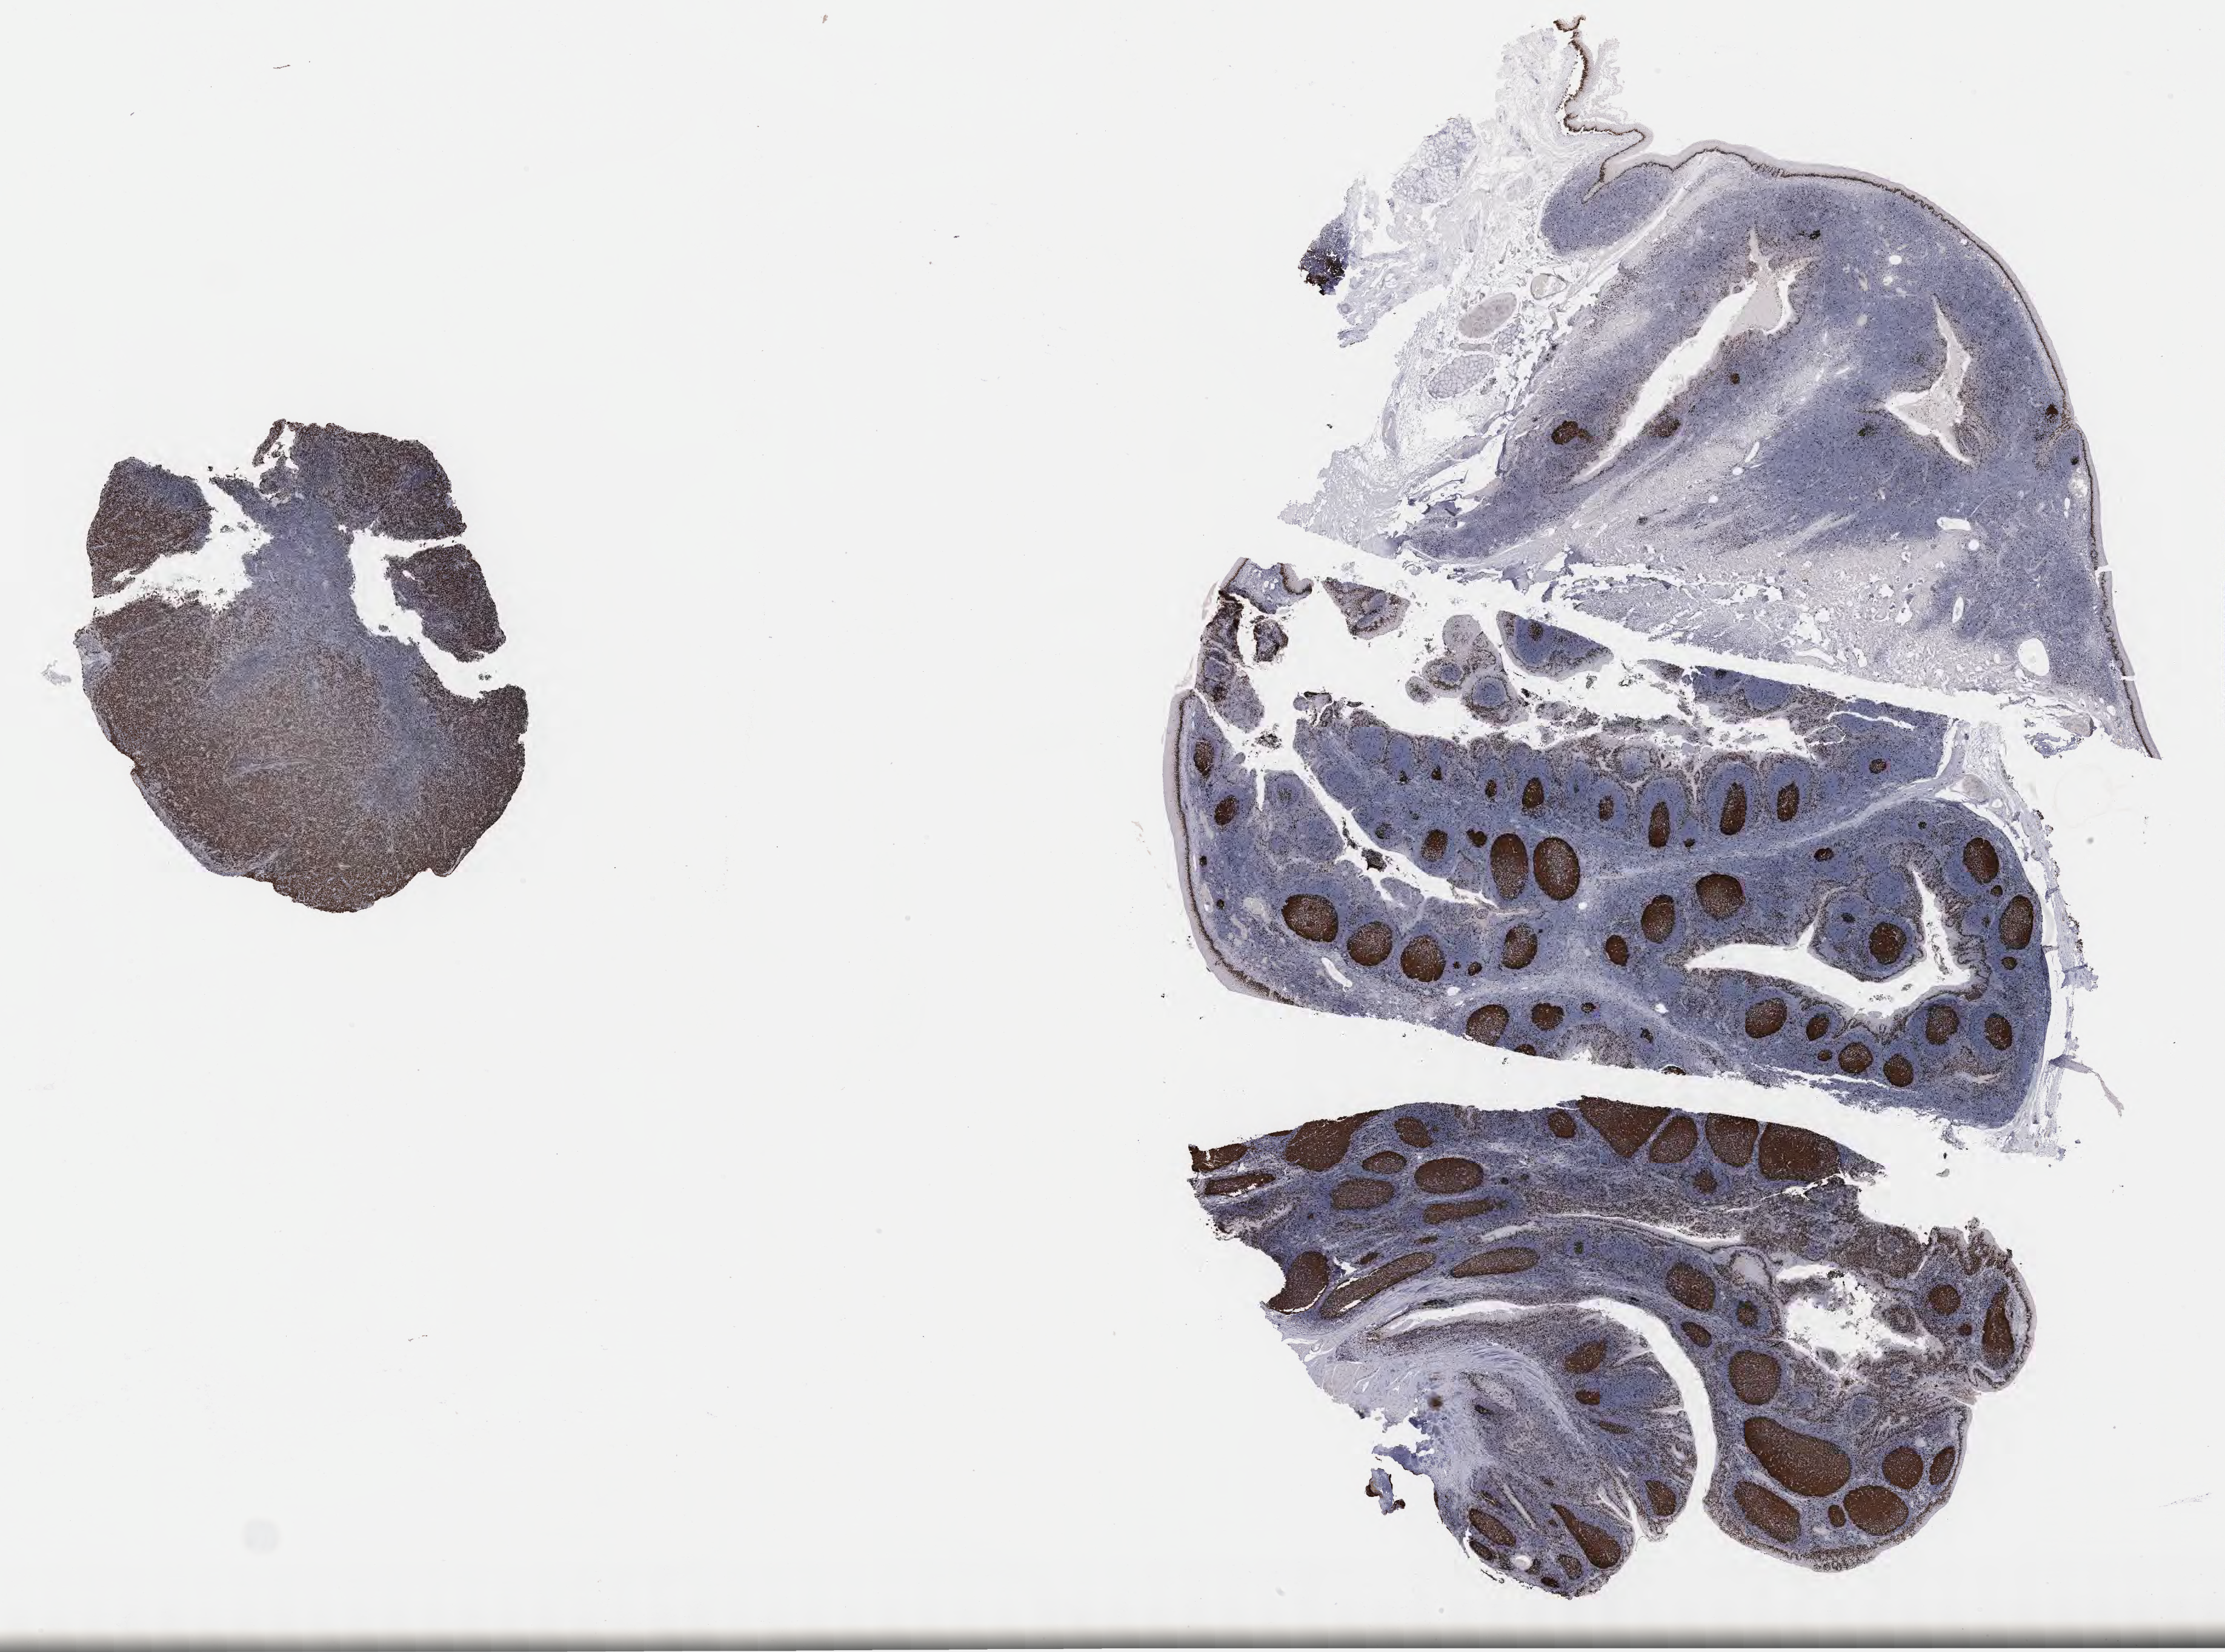
IHC for Ki-67, whole-slide image — shown as a low-resolution overview of the whole scanned area (about 29.7 x 22.1 mm). Tumor tissue. Anatomic site: liver. Patient male; 46 years old.
Histologic diagnosis: Diffuse large B-cell lymphoma, NOS.